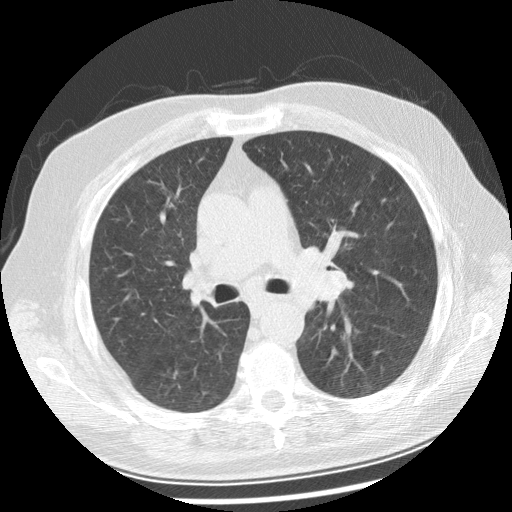
Chest CT (low-dose screening protocol), one axial image. Baseline annual screen. Lung window (W 1500 / L -600 HU). Standard (soft-tissue) reconstruction kernel (STANDARD). Slice 99 of 250 in the series. Male participant, aged 70 years at enrolment. Current smoker at enrolment.
Expert reader's lesion annotation, bounding box <279,242,360,306> (left, top, right, bottom; pixels). Screening reader's record for this exam: no non-calcified nodule ≥4 mm recorded. Participant outcome: lung cancer diagnosed 29 days after this screen — squamous cell carcinoma, keratinizing, NOS, left main stem bronchus, moderately differentiated (G2), stage IIIB (AJCC 6th edition), 40 mm at pathology.